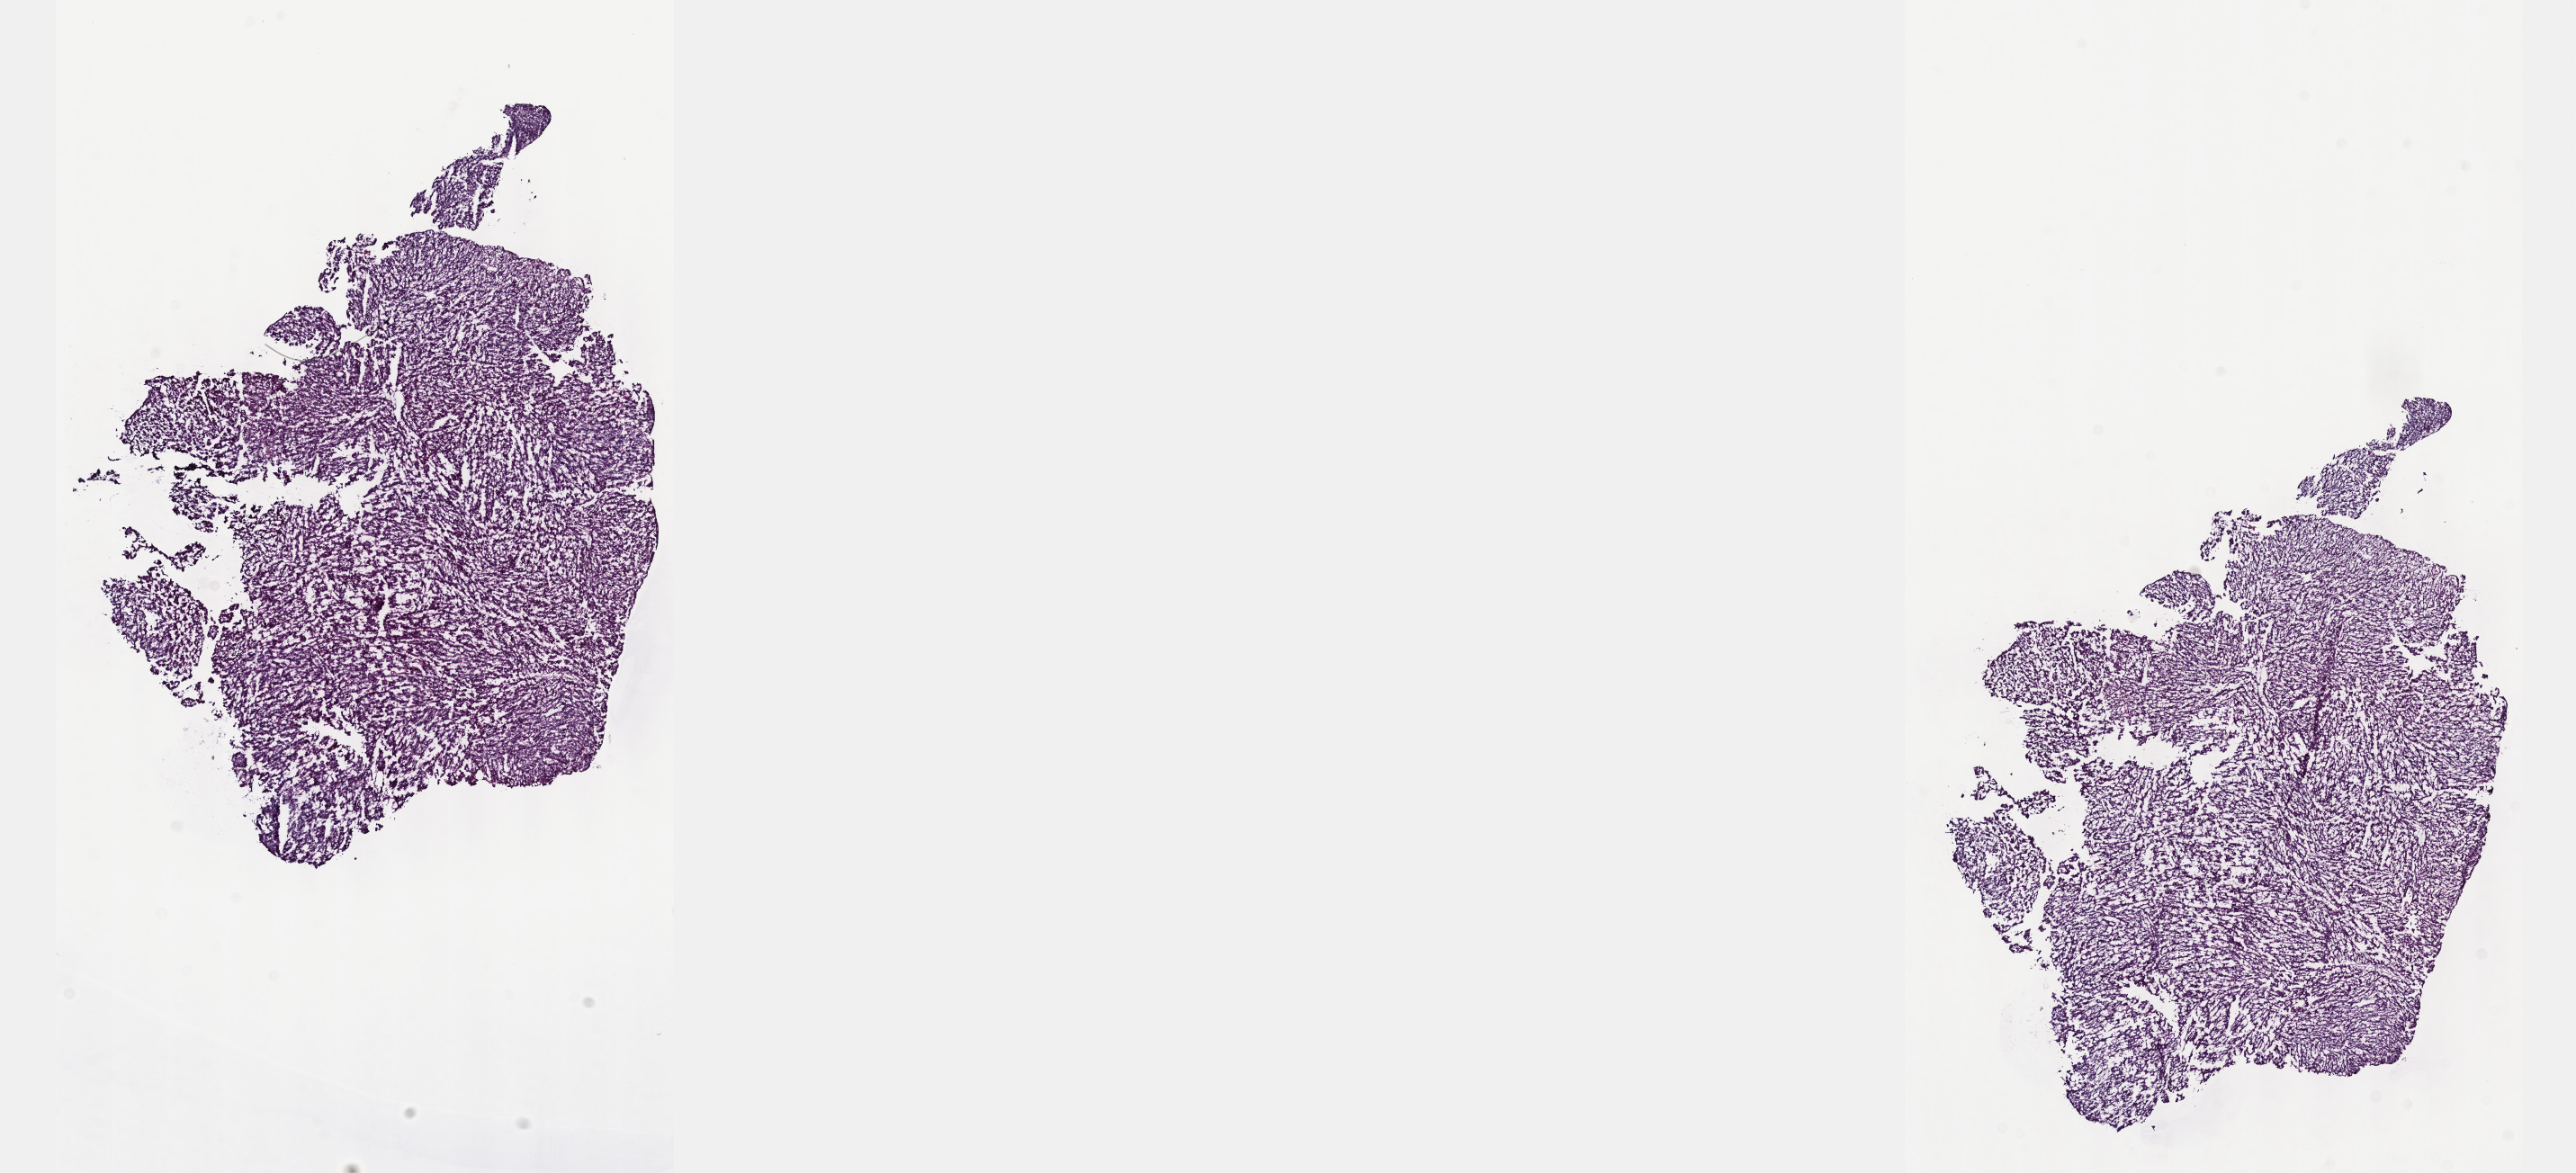
Whole-slide histology image, H&E-stained — a low-resolution overview of the entire scanned area, about 23.1 x 10.5 mm (from a 40x scan); frozen section from the top of the tissue portion; primary tumour sample from the liver. Male, age 58 years at initial diagnosis. Histologic grade: G3 (poorly differentiated). Pathologist review of this section (percent, as recorded): tumour cells 90%, tumour nuclei 95%, normal cells 0%, stromal cells 10%, necrosis 0%. Infiltration values recorded for this section: lymphocyte infiltration 0%, monocyte infiltration 0%, neutrophil infiltration 0%.
* diagnosis: Hepatocellular carcinoma, NOS
* AJCC pathologic stage: I (6th edition)